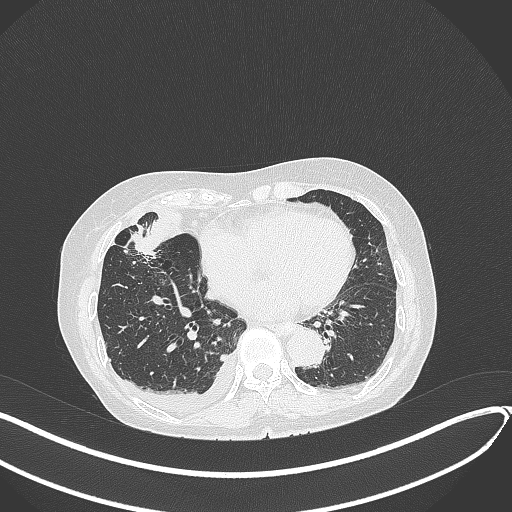
Chest CT, one axial slice. Position 140 of 418 along the scan axis. 120 kVp. Lung window (W 1500 / L -600 HU). 1 mm slice thickness. 512 × 512 image matrix. Female patient, age 75 years. From the clinical record (not read from this slice): clinical TNM (as recorded): T2a N3 M0.
Annotated regions visible in this slice (rectangle marked by the reading radiologist):
- lung tumour (recorded histology: adenocarcinoma): bounding box (x1, y1, x2, y2) in pixels: (128, 225, 161, 261)